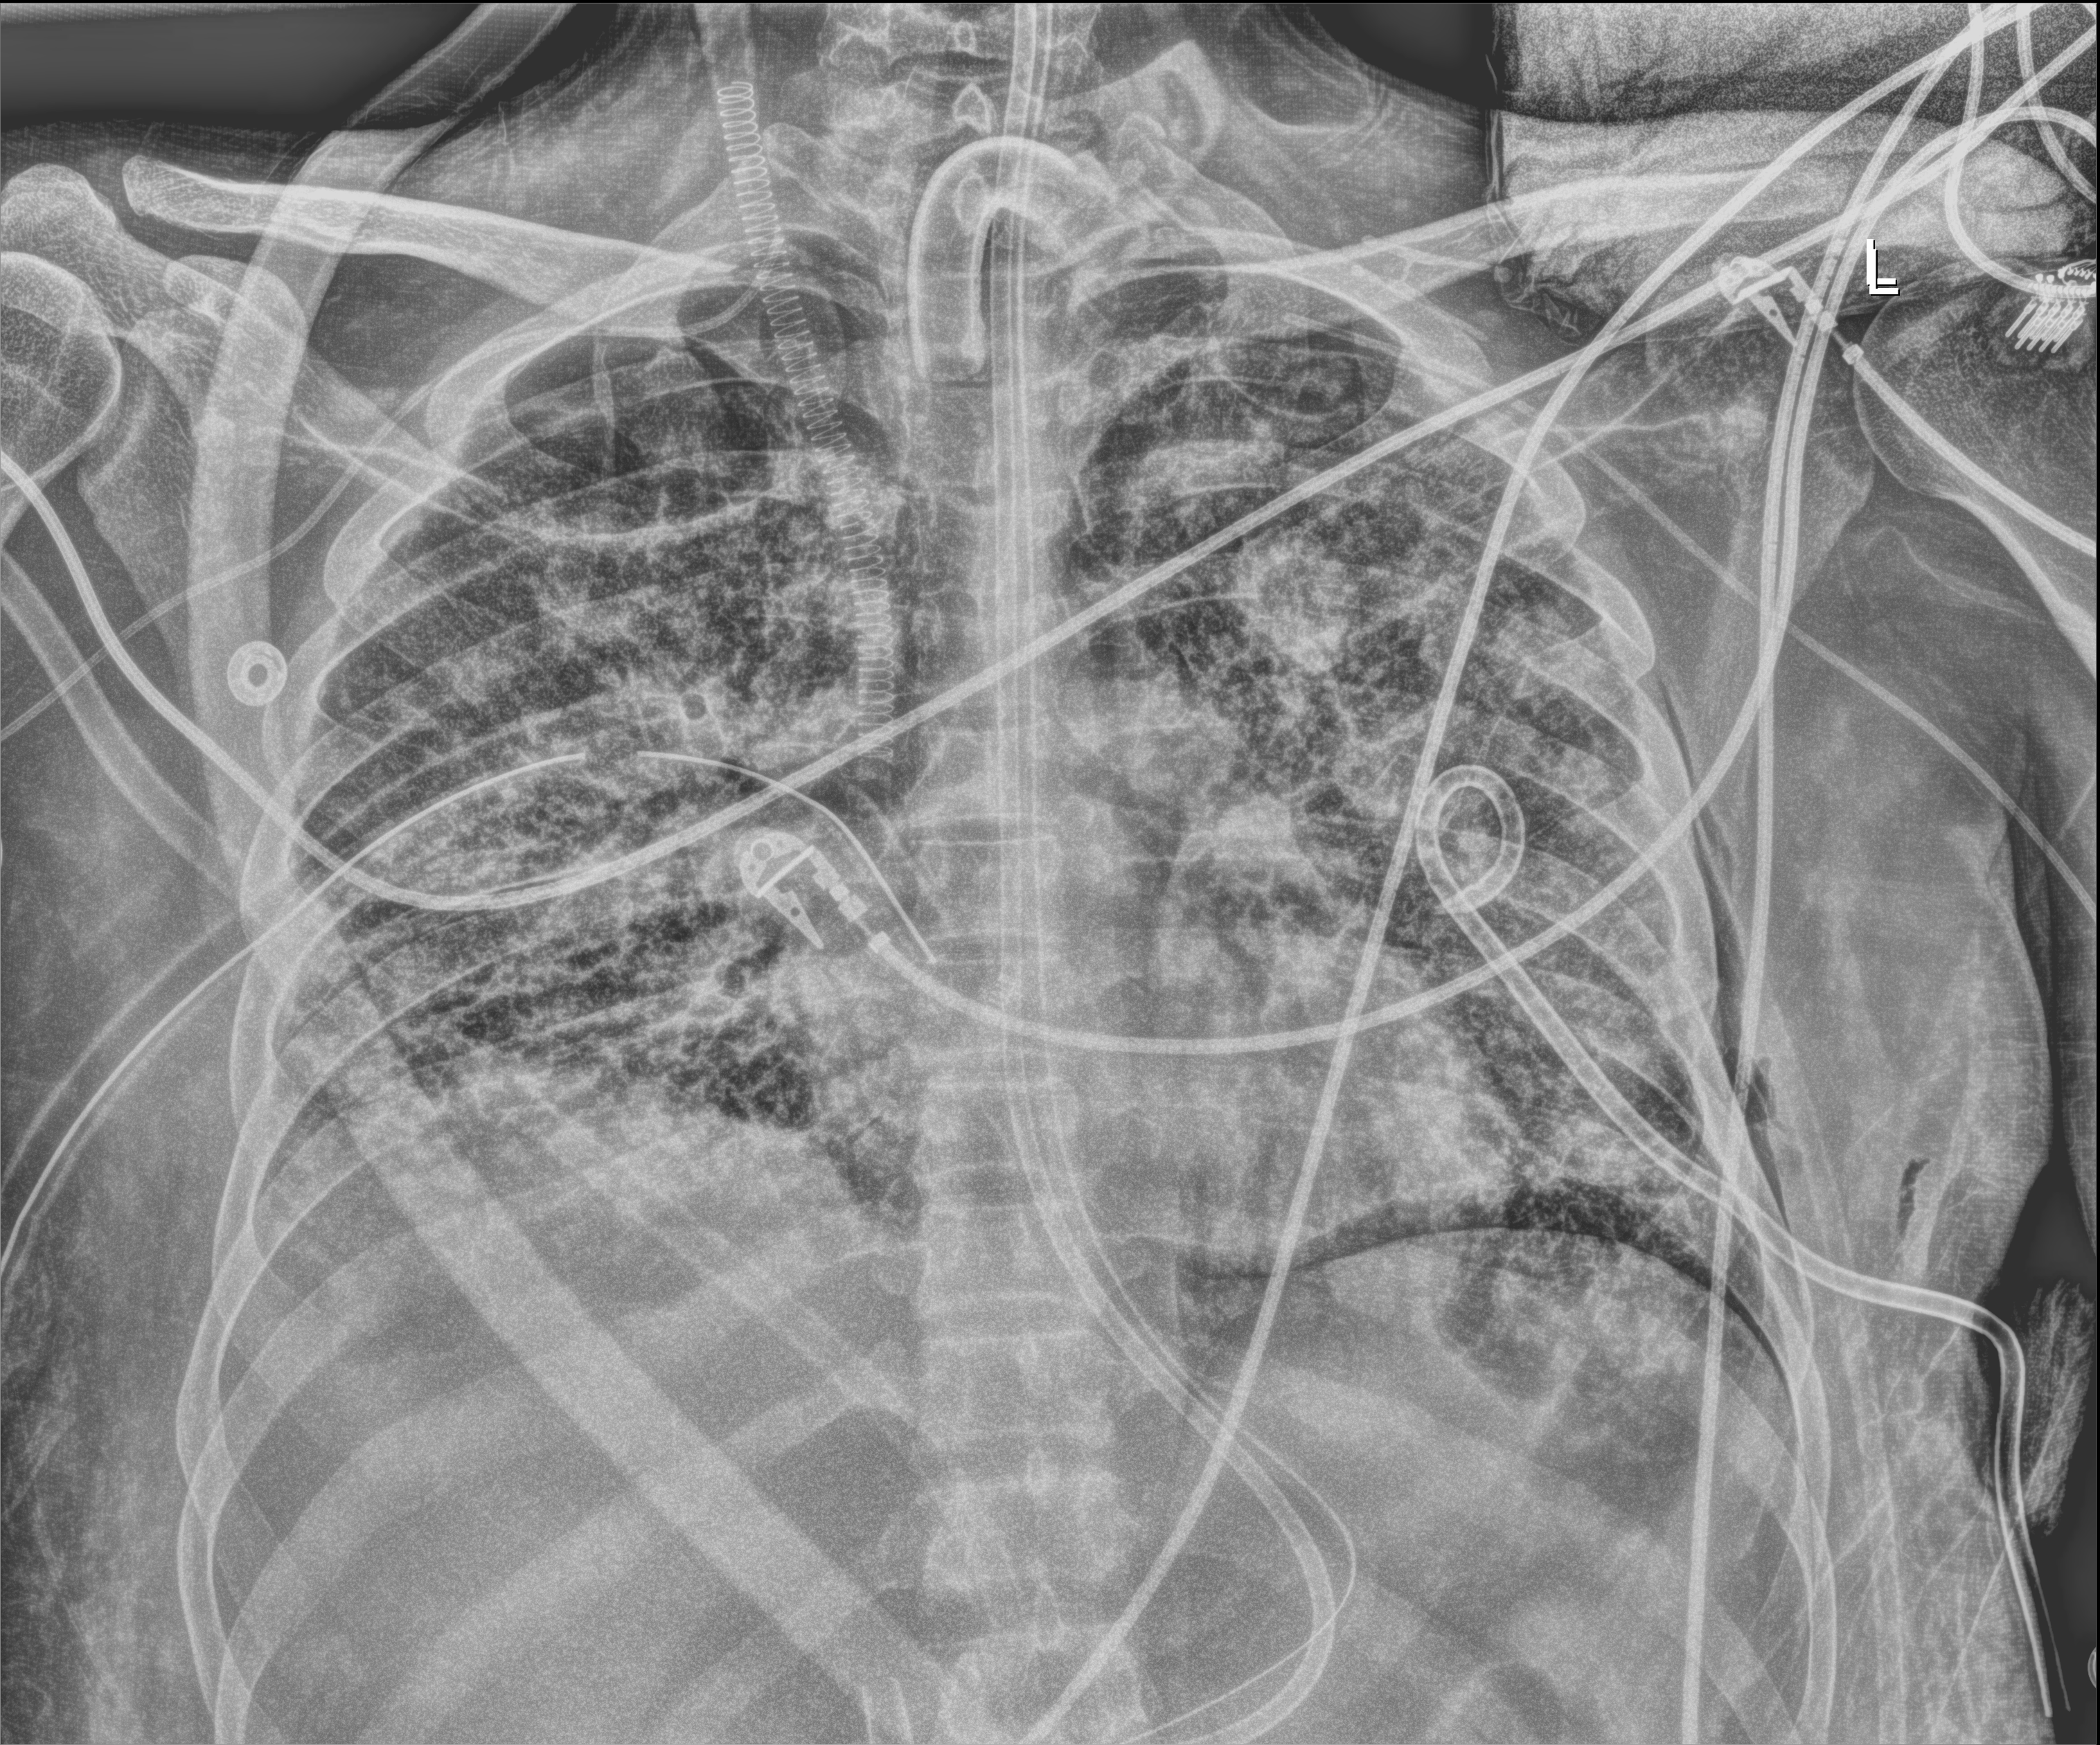
Chest X-ray; anteroposterior (AP) projection. Patient hospitalised with COVID-19, aged 18–59 years.
Hospital-stay facts (about this admission, not read from this image; timing relative to this image not recorded): mechanically ventilated during this hospital stay: yes; admitted to intensive care during this hospital stay: yes.